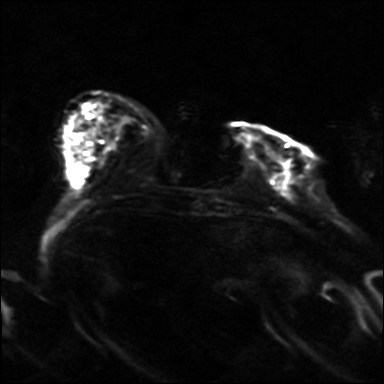
Breast MRI, one axial slice. Position 8 of 36 along the scan axis. Diffusion-weighted series; image 2 of 4 stored at this slice position (different b-values; order by instance number). 3 T. 4 mm slice thickness. 384 × 384 image matrix, field of view 320 × 320 mm. Female patient.
Outlined on this slice (manually delineated by an expert):
- tumour on diffusion-weighted imaging: bounding box [x1, y1, x2, y2] px = [285, 162, 292, 184]